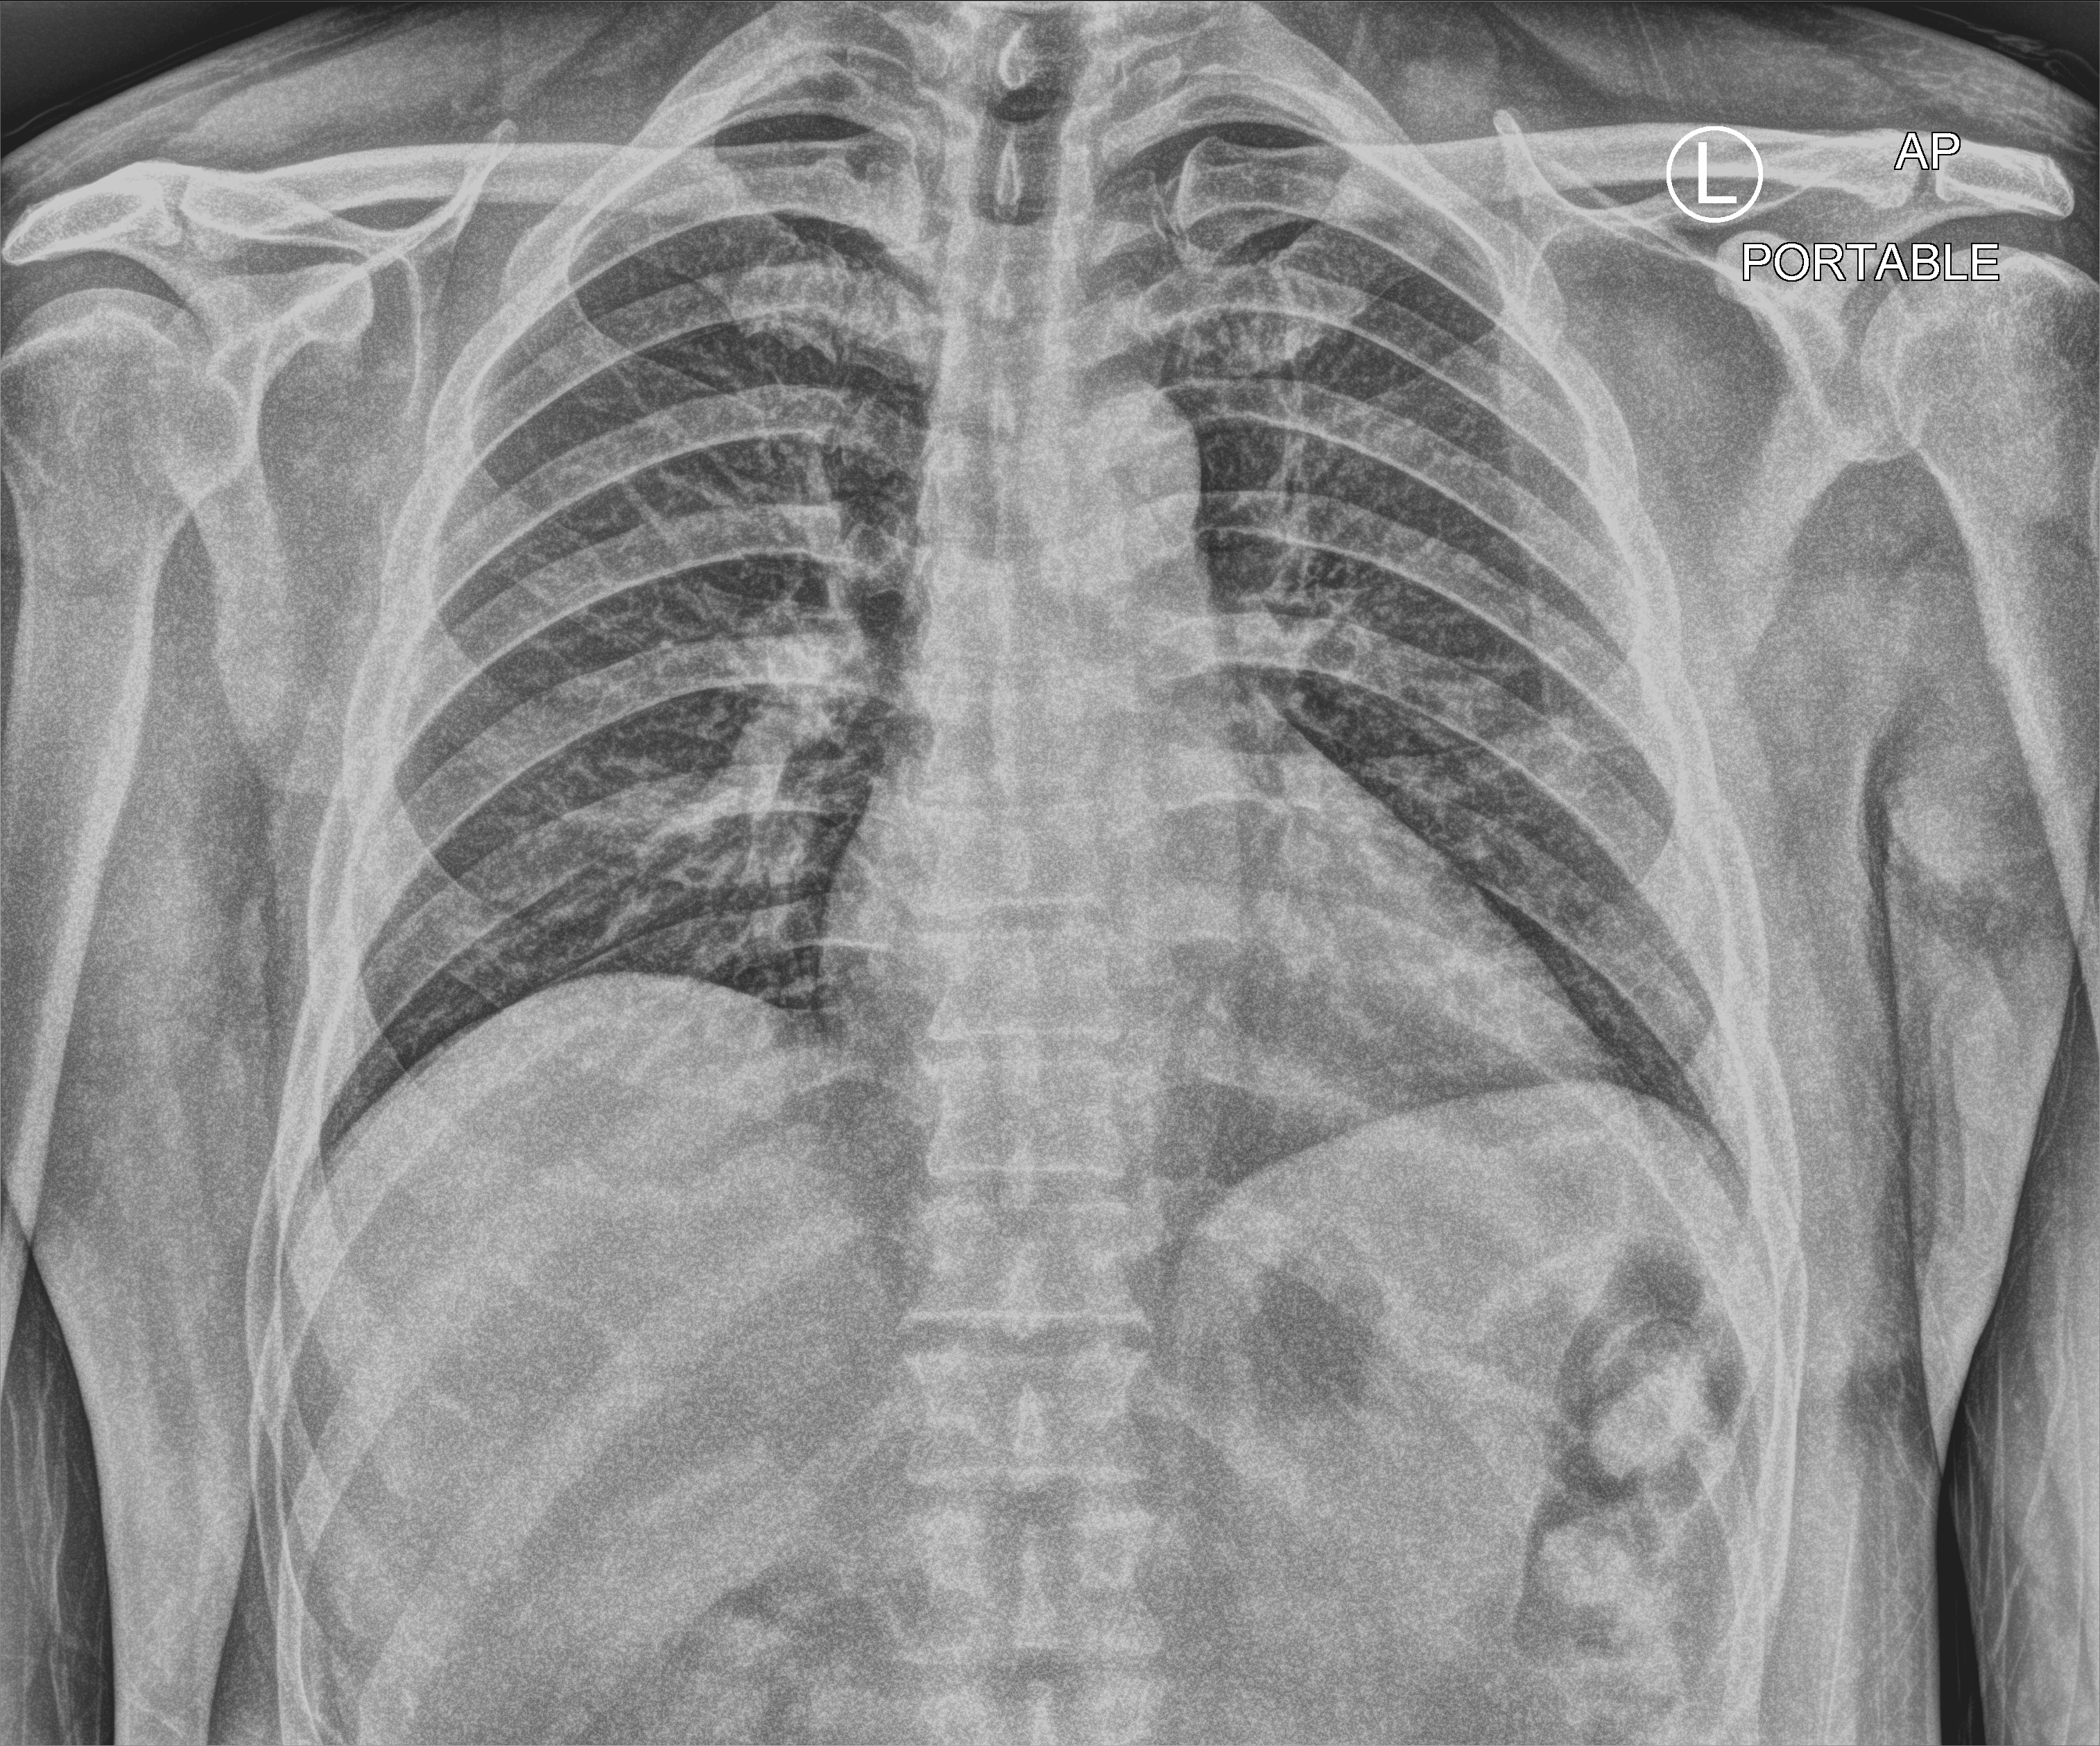
Chest X-ray (portable), anteroposterior (AP) projection. Male patient hospitalised with COVID-19, age 18–59 years.
Hospital-stay facts (about this admission, not read from this image; timing relative to this image not recorded):
- admitted to intensive care during this hospital stay: no
- chronic kidney disease (admission record): no
- mechanically ventilated during this hospital stay: no